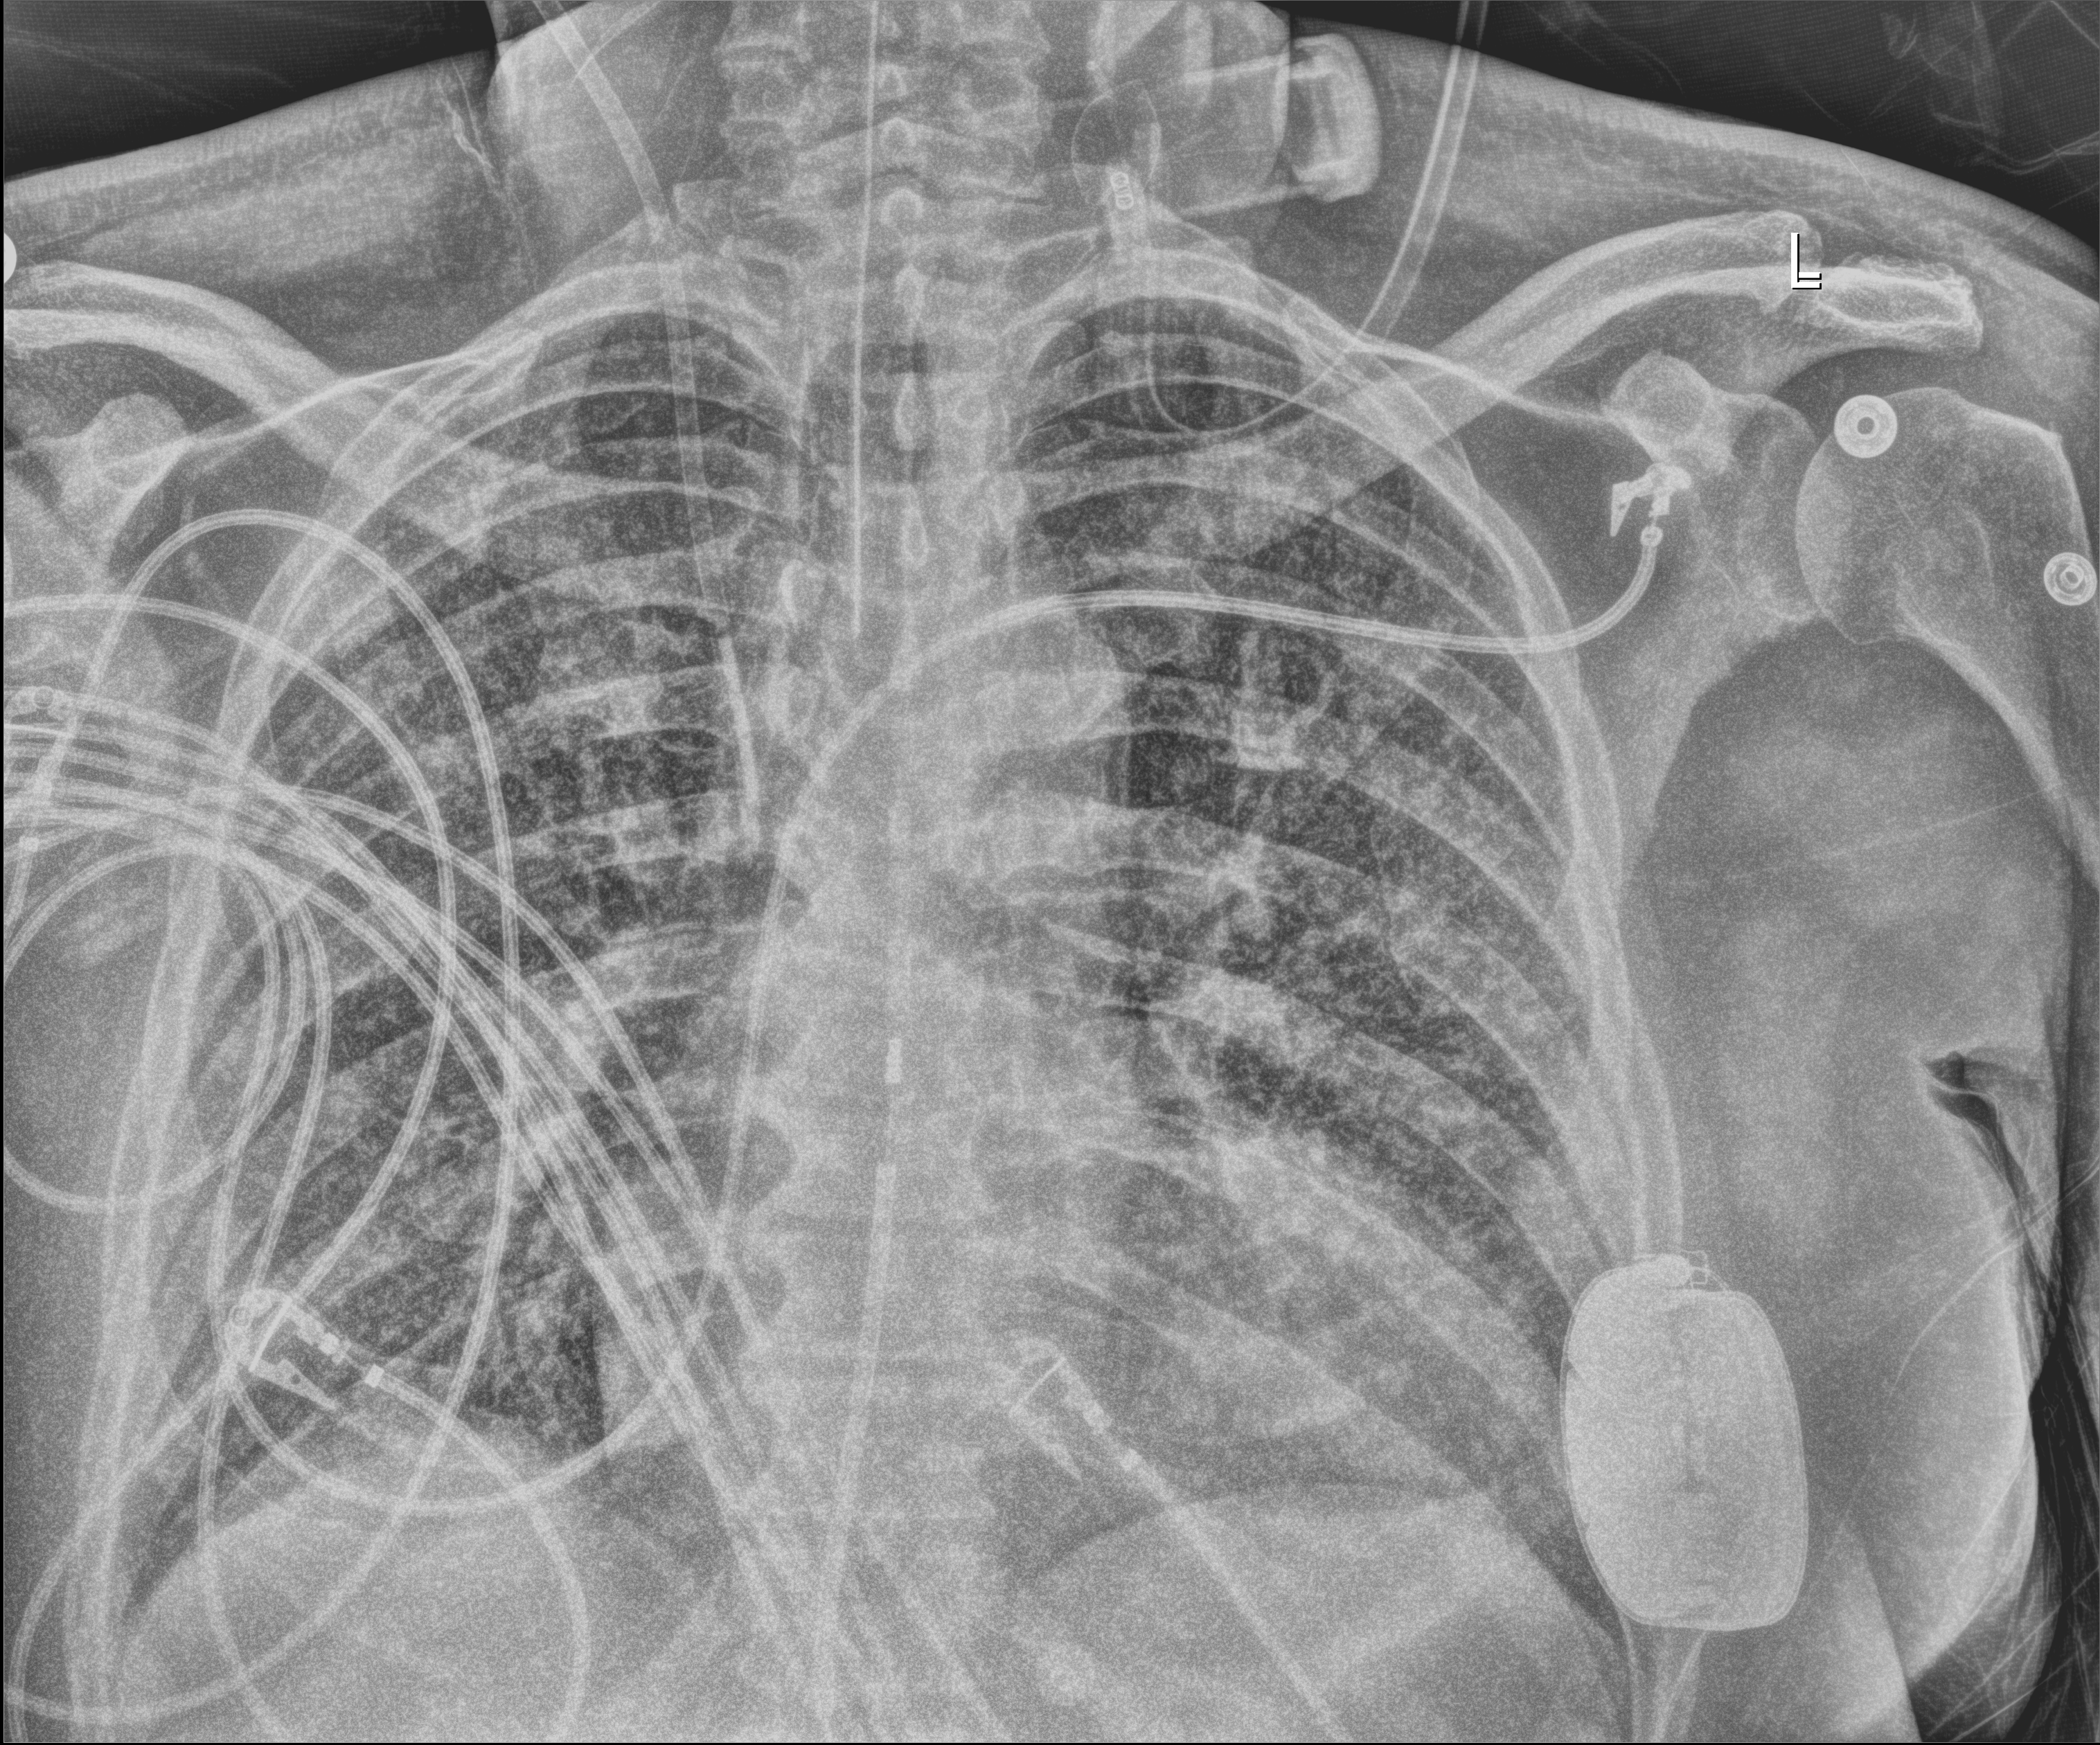
Chest X-ray (portable); anteroposterior (AP) projection. Male patient hospitalised with COVID-19, age 60–74 years.
From the hospital-stay record, not from the radiograph (when in the stay this image was taken is not recorded): mechanically ventilated during this hospital stay: yes.